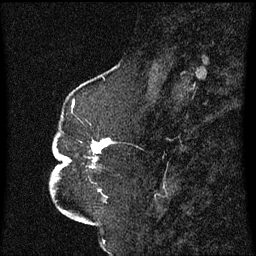
Breast MRI (dynamic contrast-enhanced), one sagittal slice. Slice 25 of 60 in the series (ordered by position). Dynamic contrast-enhanced series, image 2 of 3 at this slice position (ordered by acquisition). 1.5 T. TE 4.2 ms, TR 8.4 ms. 2.3 mm slice thickness. 256 × 256 image matrix. Female patient, age 52 years. Case-level facts recorded for this patient, not image findings: setting: breast cancer imaged before/during neoadjuvant chemotherapy; receptor status: HR-positive, HER2-negative.
Annotated regions visible in this slice (semi-automatic segmentation, software-assisted and operator-edited):
- analysis volume of interest (the breast-tissue region the enhancement analysis was run in; not a lesion): bounding box [x1, y1, x2, y2] px = [50, 124, 111, 197]
- tumour enhancement mask (voxels above the 70 % enhancement threshold inside the analysis volume of interest): [63, 138, 110, 169]